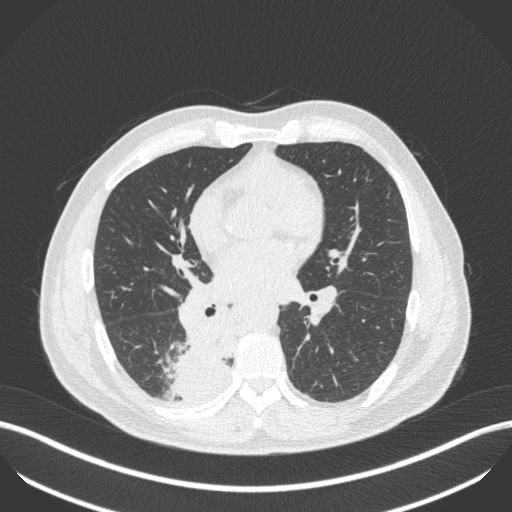
Chest CT, one axial slice; slice 231 of 451 in the series (ordered by position); reconstruction kernel B31f; 100 kVp; lung window (W 1500 / L -600 HU); 1 mm slice thickness; 512 × 512 image matrix, field of view 400 × 400 mm. Patient: male, 61 years. From the clinical record (not read from this slice): clinical TNM (as recorded): T1 N0 M0.
Annotated regions visible in this slice (rectangle marked by the reading radiologist):
- lung tumour (recorded histology: small cell carcinoma): bounding box <163,318,235,403> (left, top, right, bottom; pixels)